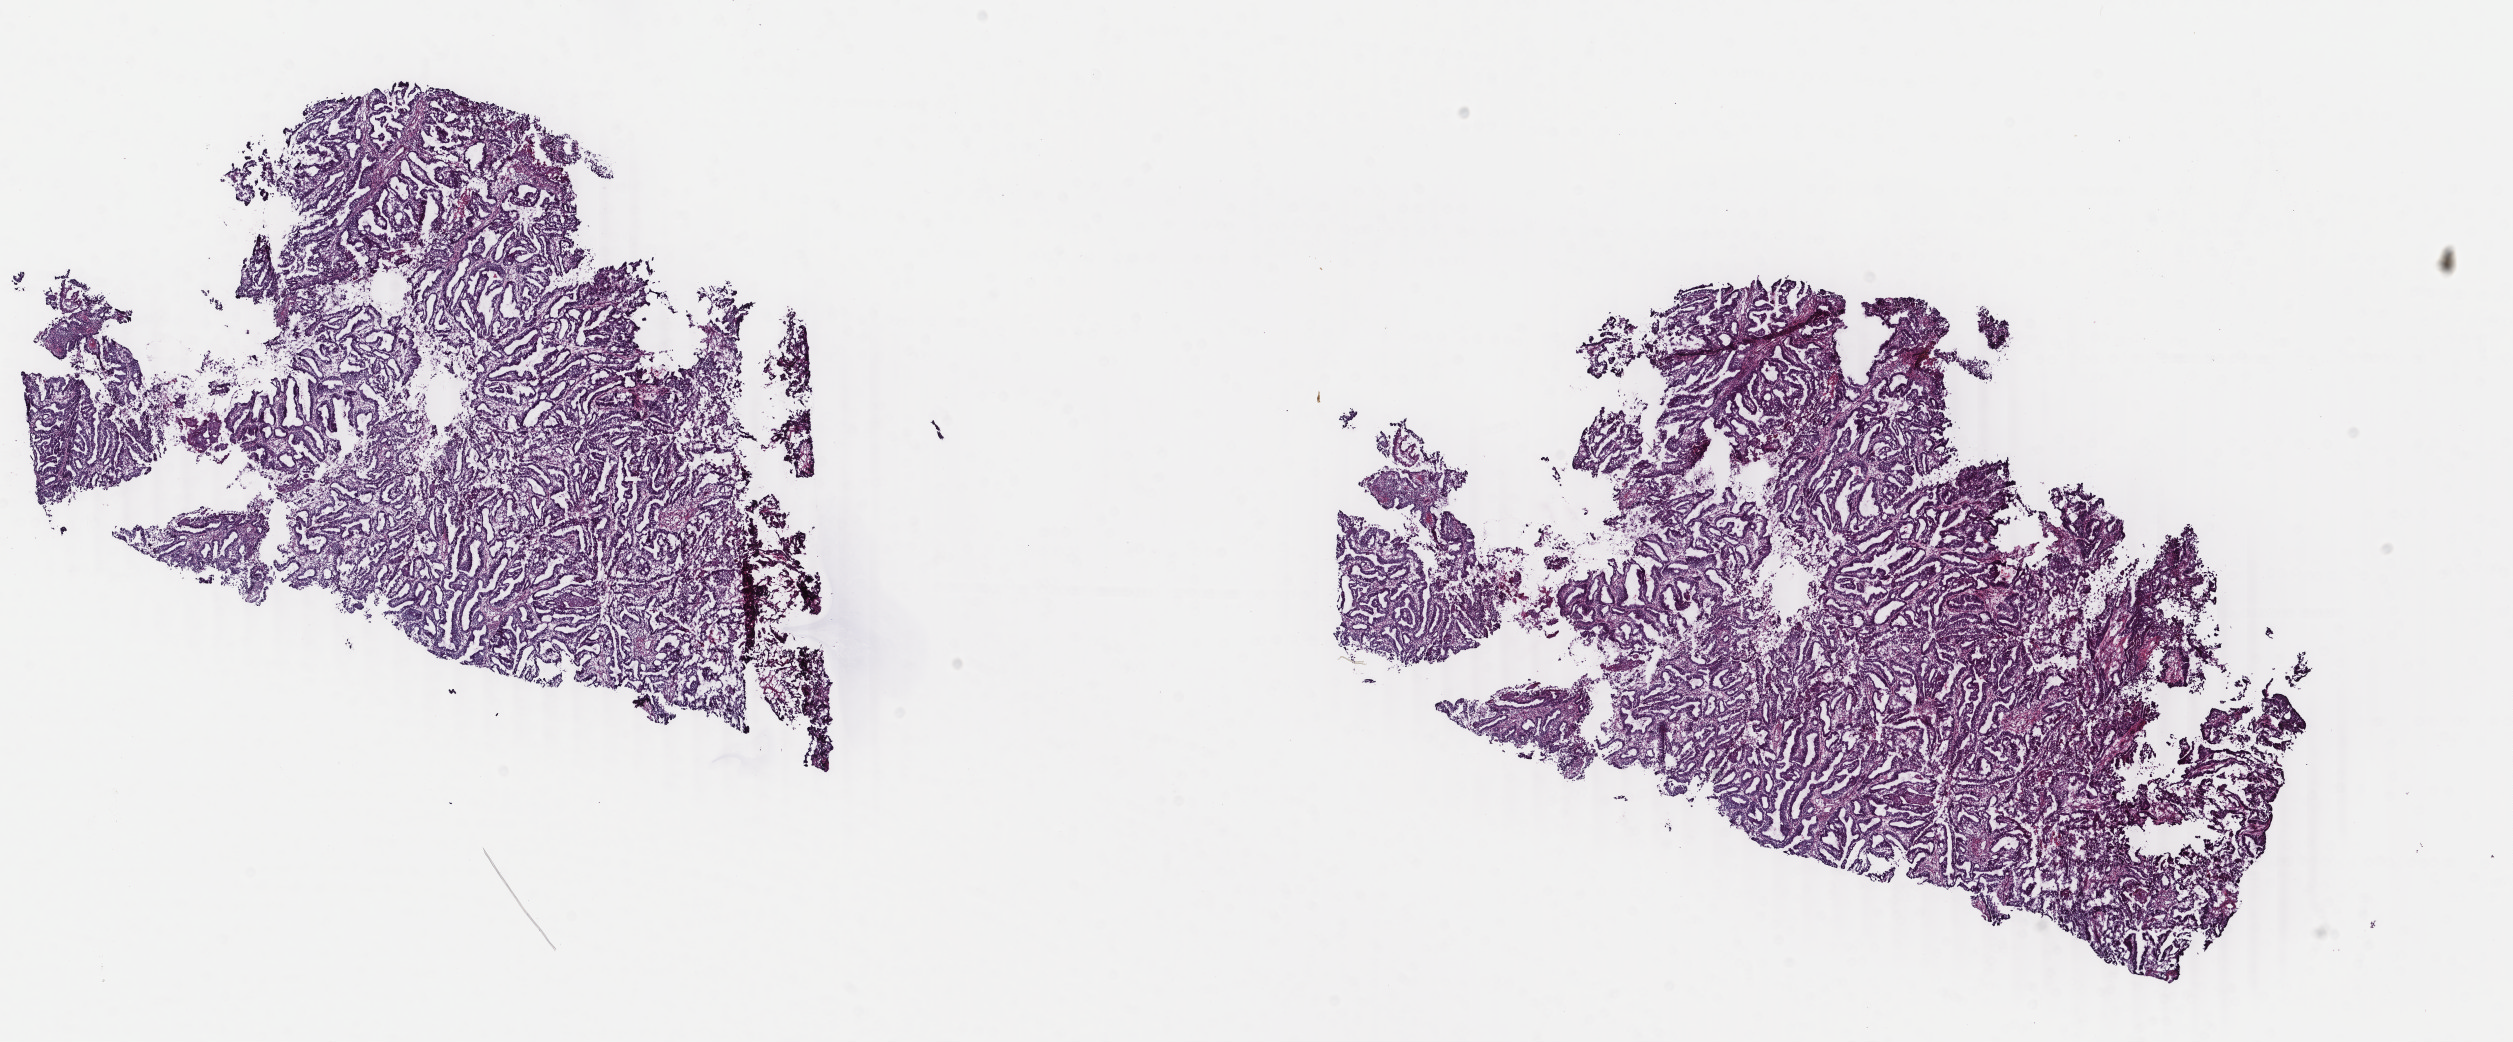
Digitized H&E tissue section (whole slide), low-resolution overview of the scanned area, about 20.0 x 8.3 mm (from a 40x scan). Frozen section. Primary tumour sample from the uterus. Female patient; age at initial diagnosis 64 years. Histologic grade: G1 (well differentiated). Pathologist review of this section (percent, as recorded): tumour cells 60%, tumour nuclei 70%, normal cells 0%, stromal cells 30%, necrosis 10%. Inflammatory infiltration, as recorded: lymphocyte infiltration 10%, monocyte infiltration 0%, neutrophil infiltration 0%.
• FIGO stage: IA
• diagnosis: Endometrioid adenocarcinoma, NOS (endometrium)